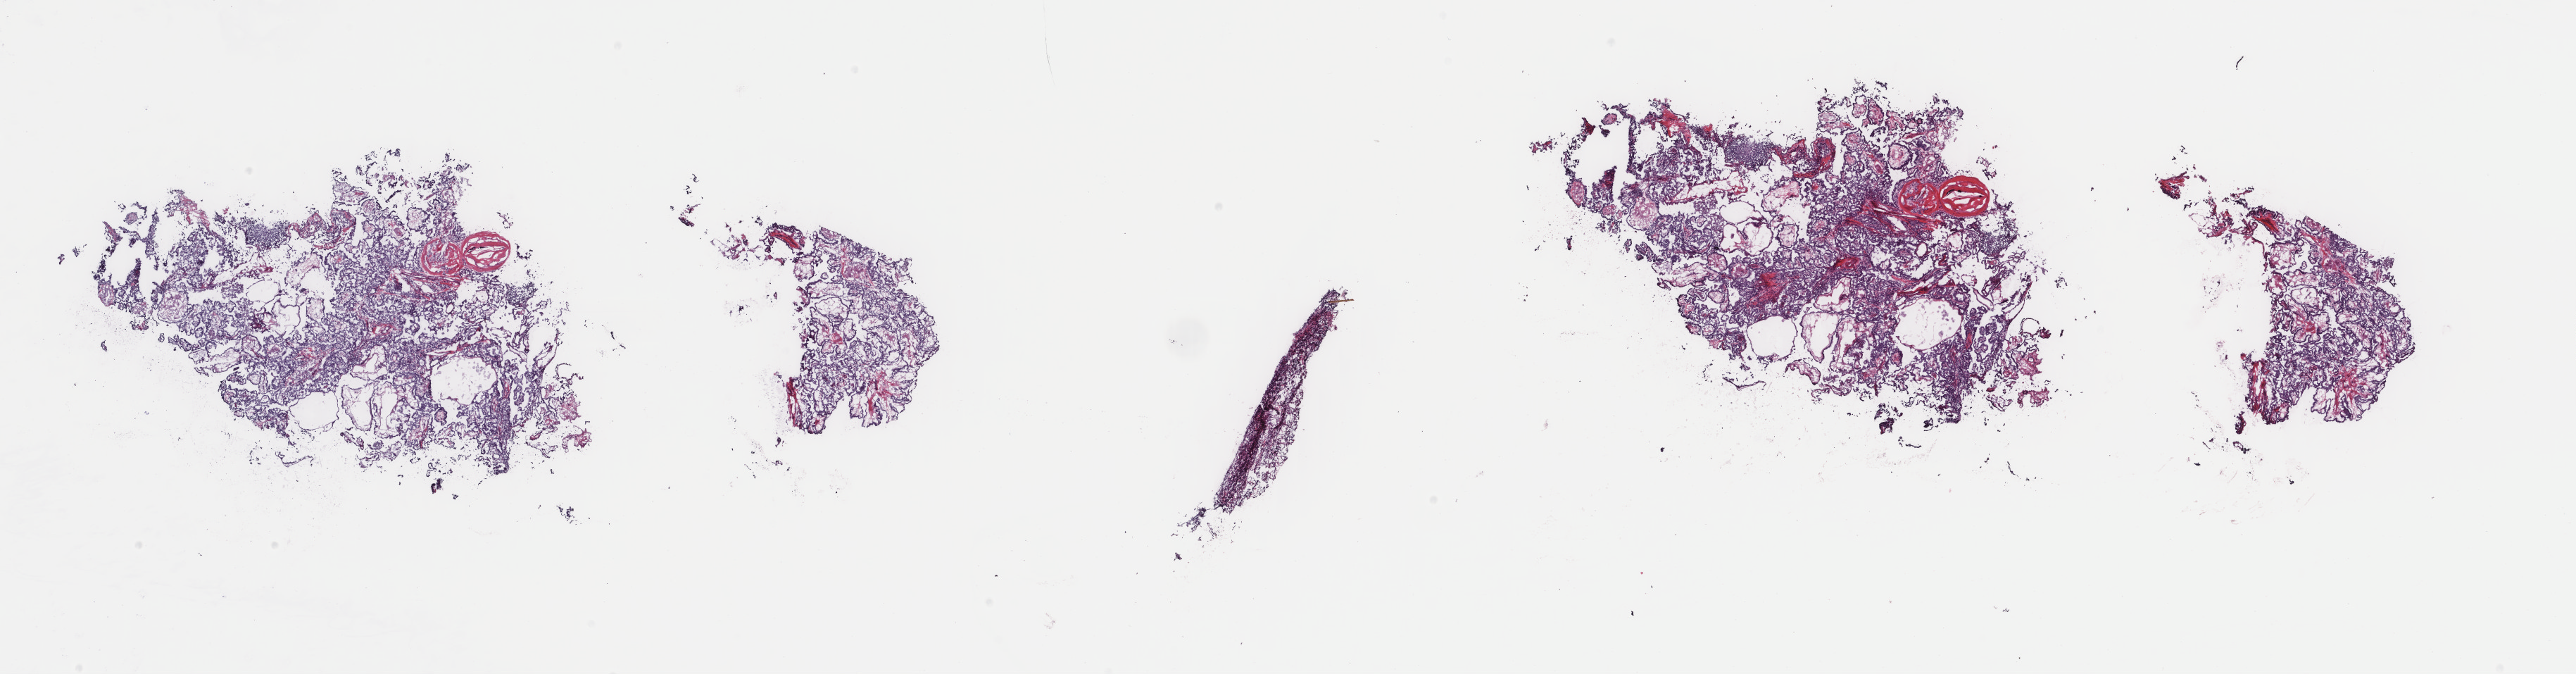
Digitized H&E-stained tissue section (whole slide), a low-resolution overview of the entire scanned area, about 29.0 x 7.6 mm (acquisition: 40x scan). Frozen section. Thyroid, primary tumour sample. Patient: female, age at initial diagnosis 58 years. Slide review estimates, as recorded: tumour cells 100%, tumour nuclei 85%, normal cells 0%, stromal cells 0%, necrosis 0%. Infiltration values recorded for this section: lymphocyte infiltration 0%, monocyte infiltration 0%, neutrophil infiltration 0%.
Diagnosis: Papillary adenocarcinoma, NOS (thyroid gland). AJCC pathologic stage: I (6th edition).